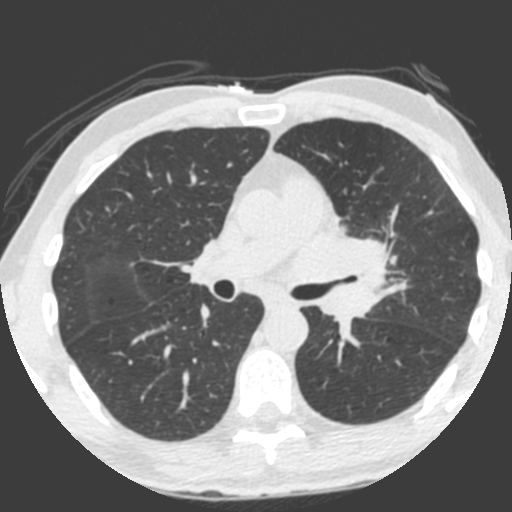
Chest CT (low-dose screening protocol), one axial image, third screening round (two years after baseline), lung window (W 1500 / L -600 HU), 2 mm slice thickness, standard (soft-tissue) reconstruction kernel (B), slice 130 of 212 in the series. Male participant, aged 55 years at enrolment. Current smoker at enrolment.
• Expert reader's lesion annotation, box from (x=309, y=213) to (x=400, y=325) px.
• The exam's reader record, not a measurement of the box and not confirmed to be the same lesion: non-calcified nodule or mass ≥4 mm, left upper lobe, 49 × 29 mm, spiculated (stellate) margins, soft tissue attenuation, pre-existing on the prior screen: yes; interval growth: yes.
• Official screen result: positive, other.
• Lung cancer was diagnosed 0 days after this screen: small cell carcinoma, NOS, left upper lobe, undifferentiated (G4), stage IV (AJCC 6th edition), 60 mm at pathology.